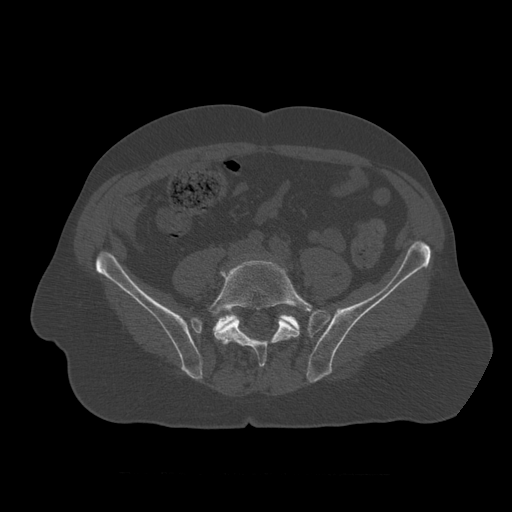
CT including the spine, one axial slice; position 253 of 450 along the scan axis; reconstruction kernel STANDARD; 120 kVp; bone window (W 1800 / L 400 HU); 1.25 mm slice thickness; 512 × 512 image matrix, field of view 405 × 405 mm. Patient age 75 years. Case-level facts recorded for this patient, not image findings: primary cancer: prostate.
Outlined on this slice (semi-automatically segmented with operator editing):
- L5 vertebra: box from (x=209, y=260) to (x=322, y=367) px